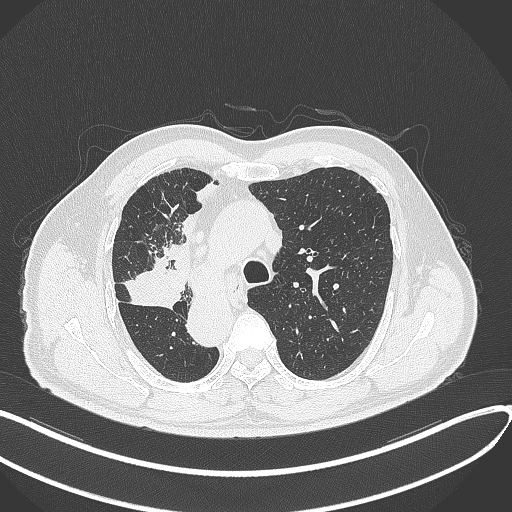
Chest CT, one axial slice; slice 221 of 300 in the series (ordered by position); reconstruction kernel B70f; lung window (W 1500 / L -600 HU); 1 mm slice thickness; 512 × 512 image matrix, field of view 400 × 400 mm. Patient: male, 67 years. From the clinical record (not read from this slice): clinical TNM (as recorded): T2a N0 M0.
Structures marked on this image (rectangle marked by the reading radiologist):
- lung tumour (recorded histology: squamous cell carcinoma): bounding box [x1, y1, x2, y2] px = [120, 254, 190, 312]